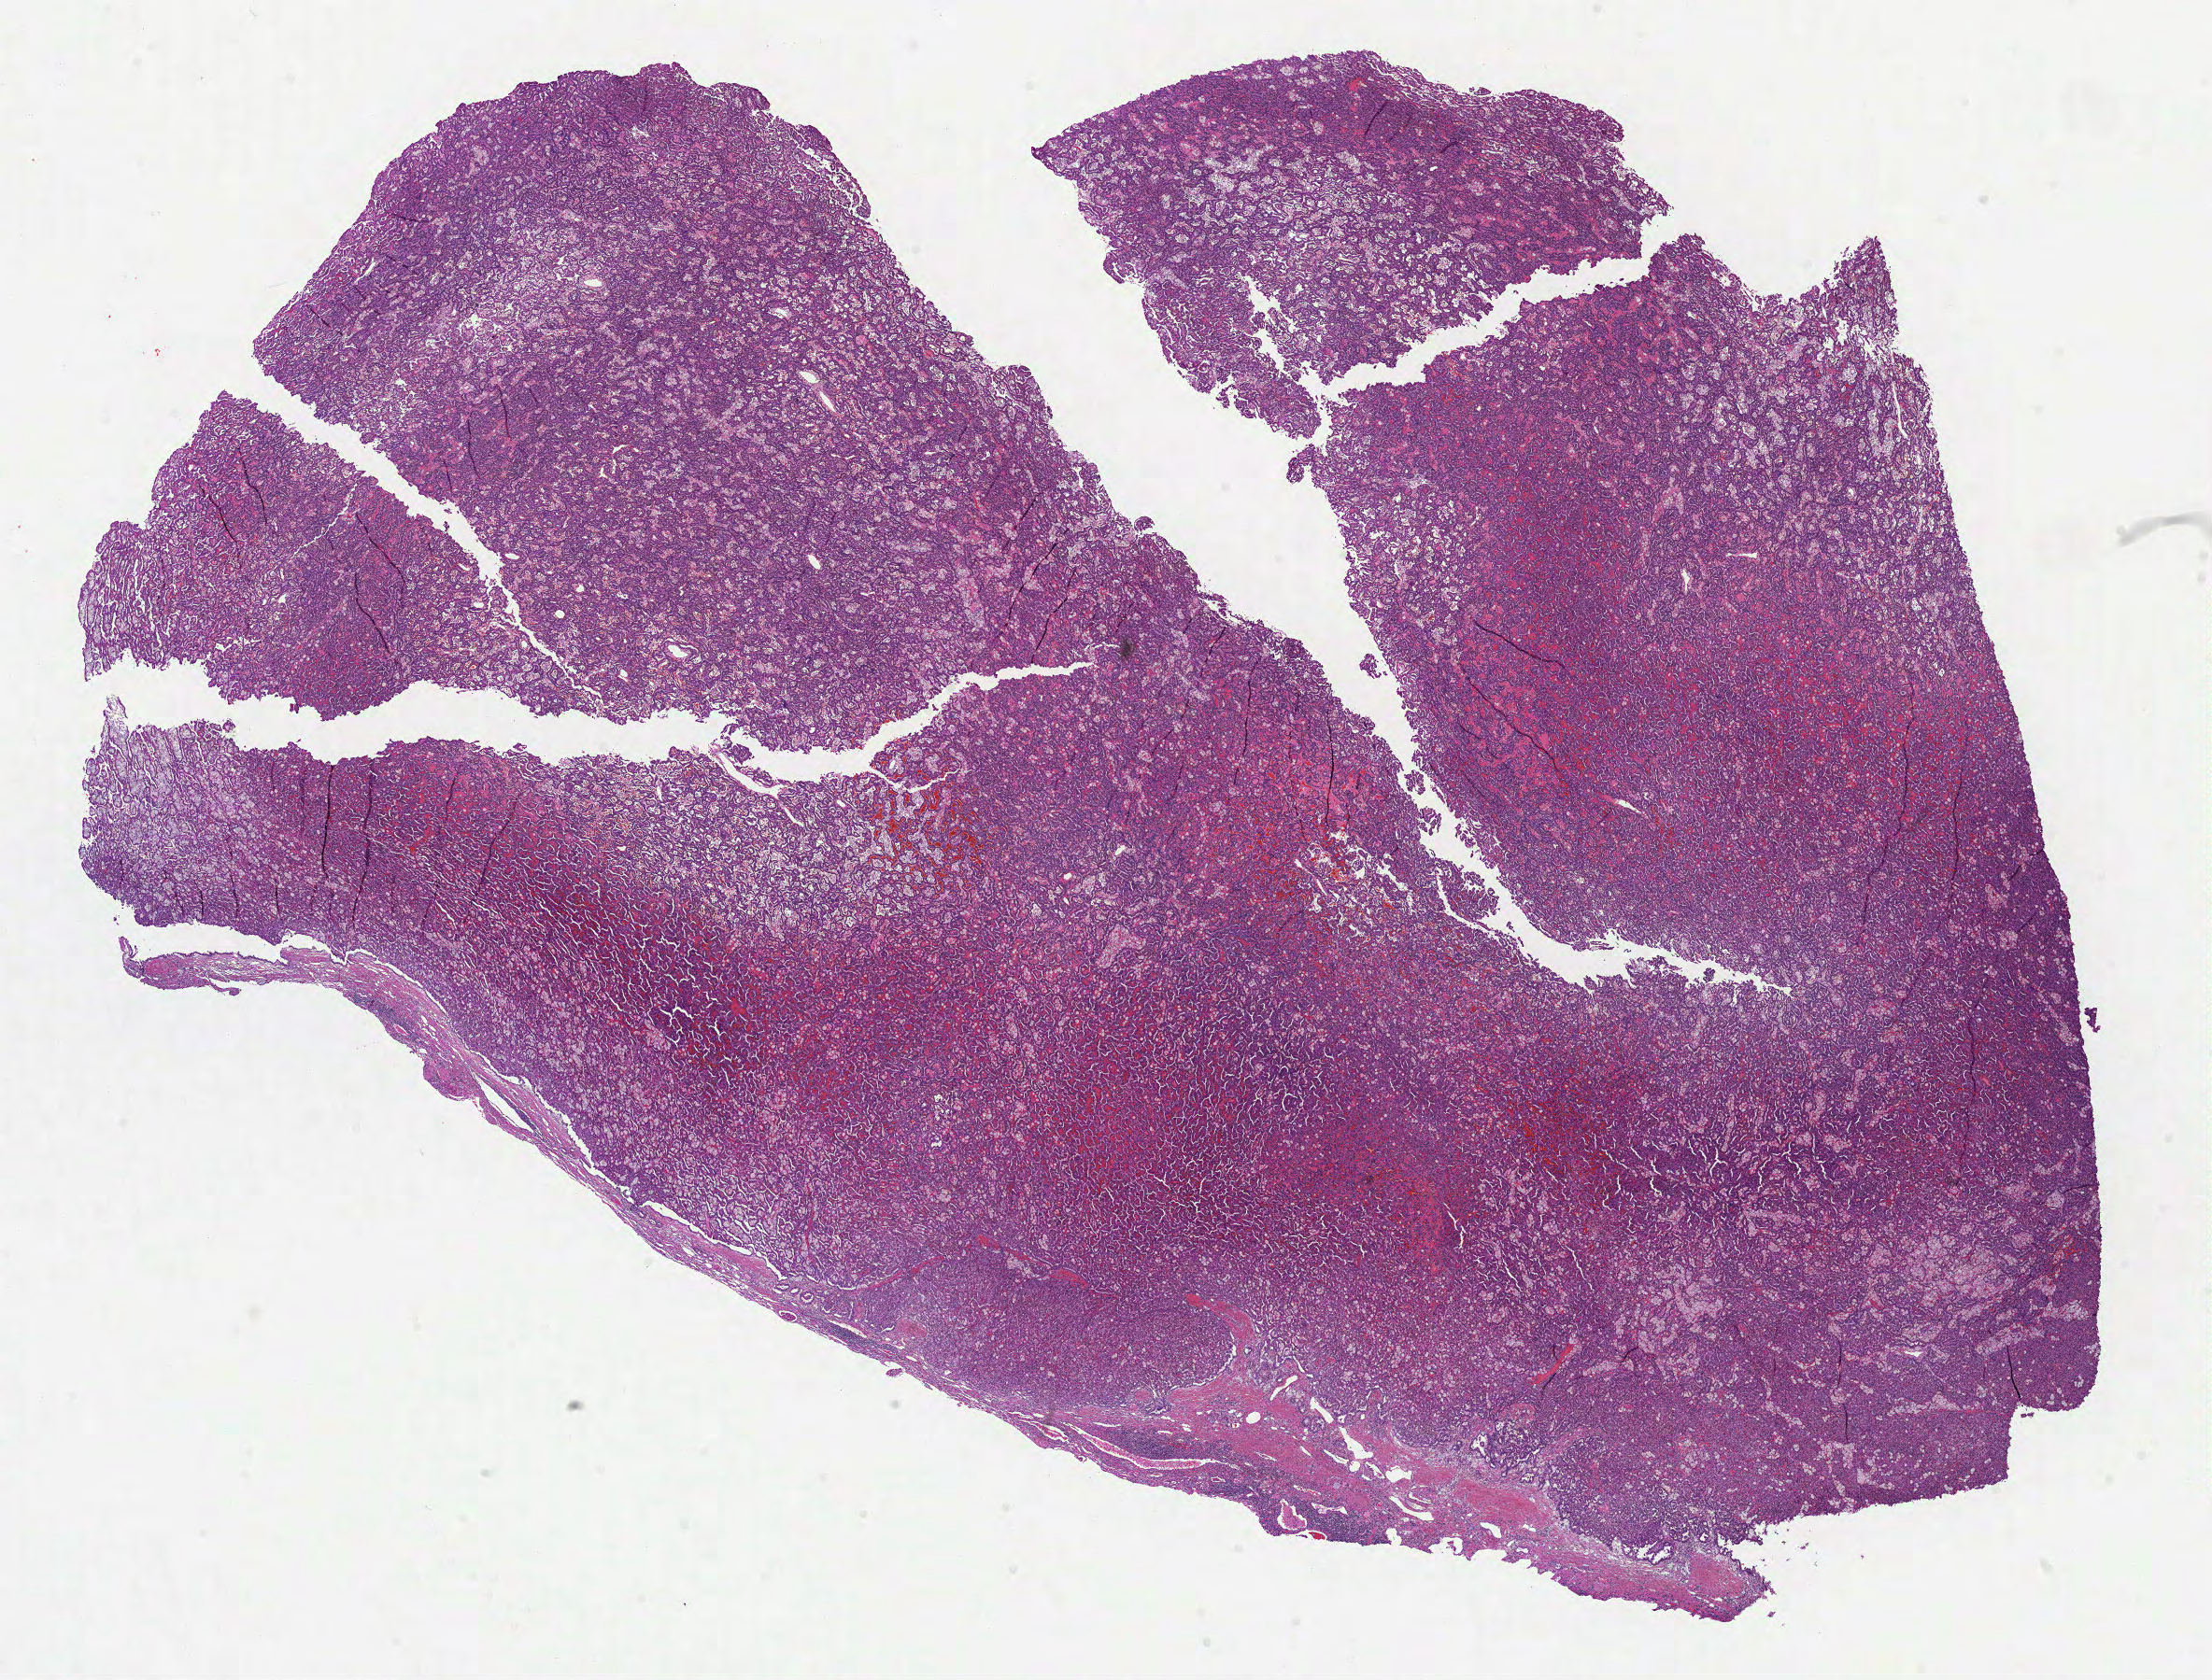
Whole-slide histology image, H&E-stained, shown as a low-resolution overview of the whole scanned area (about 19.1 x 14.5 mm, from a 40x scan). Formalin-fixed paraffin-embedded (FFPE) diagnostic section. Sample: primary tumour, kidney. Patient: male, age at initial diagnosis 43 years.
AJCC pathologic stage: I (6th edition). Laterality: right. Pathologic diagnosis: Papillary adenocarcinoma, NOS. TNM: T1b NX MX.